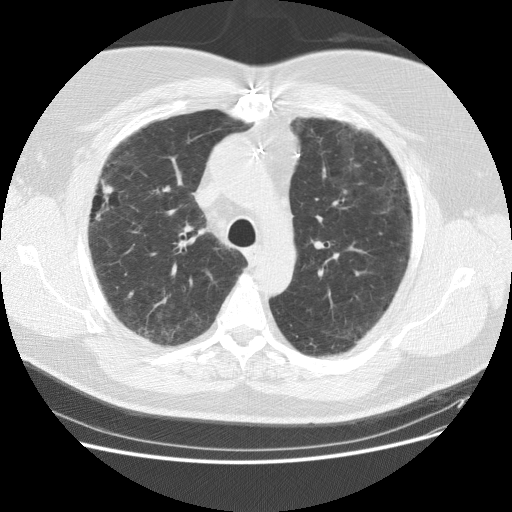
Low-dose screening chest CT, axial slice. Baseline screening round. Lung window (W 1500 / L -600 HU). 2.5 mm slice thickness. Standard (soft-tissue) reconstruction kernel (STANDARD). 512 × 512 image matrix. Male participant, aged 59 years at enrolment. Current smoker at enrolment.
- Expert-annotated lung lesion, bounding box [x1, y1, x2, y2] px = [76, 159, 134, 245].
- The screening reader recorded 2 non-calcified nodules or masses ≥4 mm on this exam; which of them this box marks is not recorded.
- Official screen result: positive, change unspecified: nodule(s) >= 4 mm or enlarging nodule(s), mass(es), or other non-specific abnormalities suspicious for lung cancer.
- Participant outcome: lung cancer diagnosed 338 days after this screen — adenocarcinoma, NOS, right upper lobe, right middle lobe, moderately differentiated (G2), stage IA (AJCC 6th edition), 13 mm at pathology.